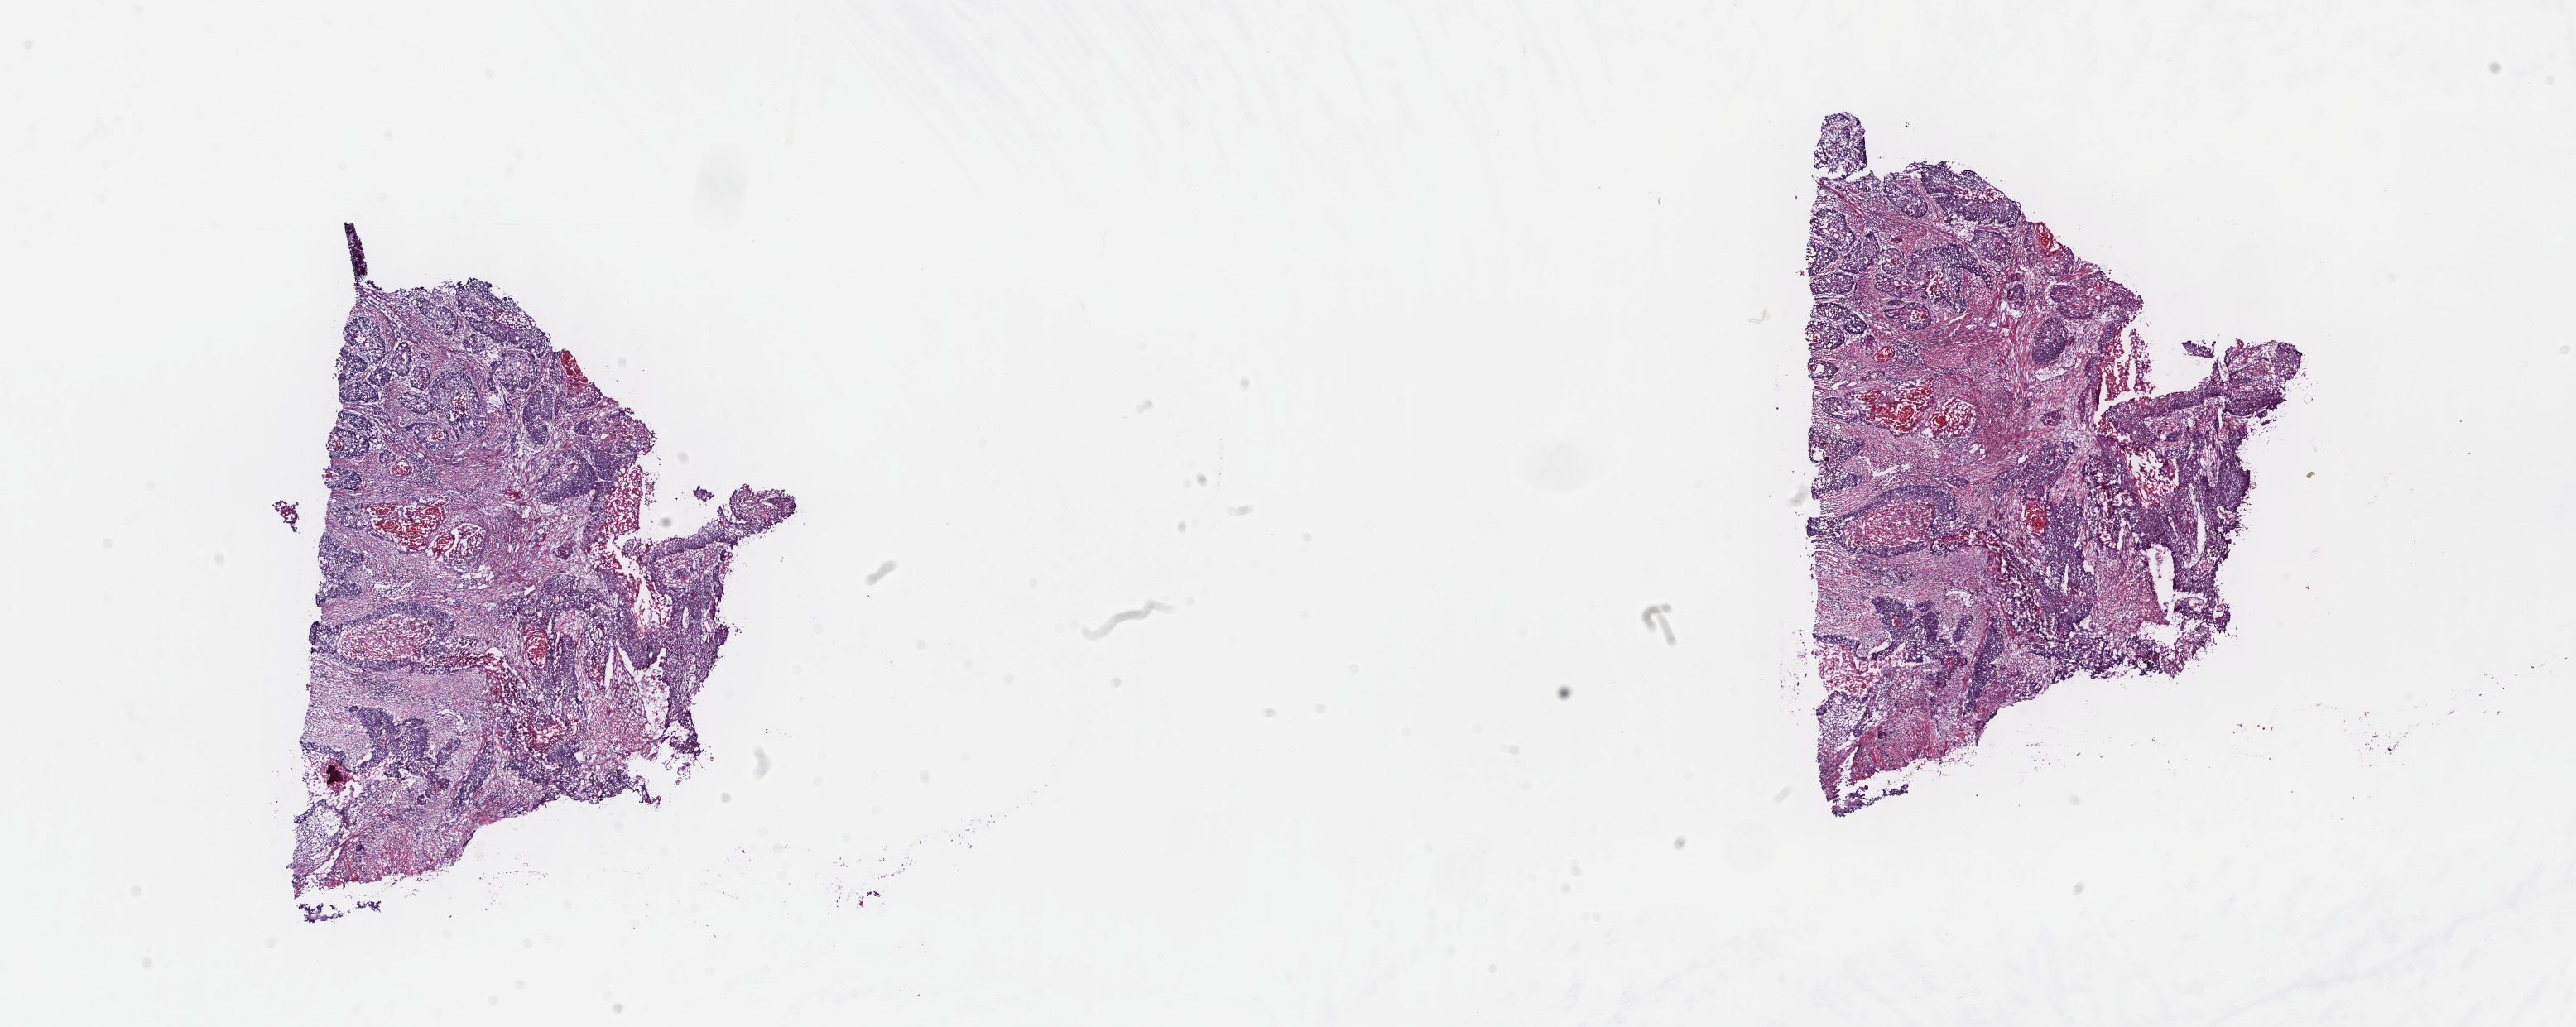
Digitized H&E-stained tissue section (whole slide) — low-resolution overview of the scanned area, about 25.2 x 10.0 mm (acquisition: 40x scan), frozen section from the top of the tissue portion, primary tumour sample from the esophagus. Patient: male, age at initial diagnosis 52 years. Histologic grade: G2 (moderately differentiated). Pathologist review of this section (percent, as recorded): tumour cells 25%, tumour nuclei 65%, normal cells 0%, stromal cells 60%, necrosis 15%. Inflammatory infiltration, as recorded: lymphocyte infiltration 20%, monocyte infiltration 3%, neutrophil infiltration 3%.
Pathologic diagnosis: Squamous cell carcinoma, NOS (lower third of esophagus). AJCC pathologic stage: IIA.